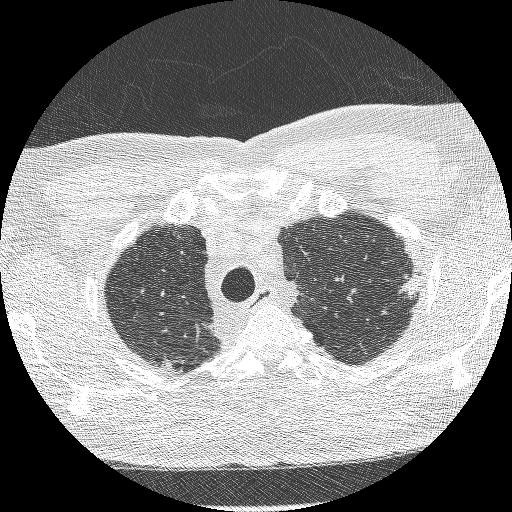
Low-dose screening chest CT, axial slice, third screening round (two years after baseline), lung window (W 1500 / L -600 HU), slice 239 of 275 in the series, 512 × 512 image matrix. Male, age 66 years at enrolment.
Expert reader's lesion annotation, bounding box [x1, y1, x2, y2] px = [388, 269, 432, 313]. Reader record for this screening exam (exam-level; its link to the box is not recorded): non-calcified nodule or mass ≥4 mm, left lower lobe, 15 × 9 mm, spiculated (stellate) margins, soft tissue attenuation, pre-existing on the prior screen: yes; interval growth: yes. Official screen result: positive, other. Participant outcome: lung cancer diagnosed 225 days after this screen — adenocarcinoma, NOS, left upper lobe, poorly differentiated (G3), stage IB (AJCC 6th edition), 16 mm at pathology.